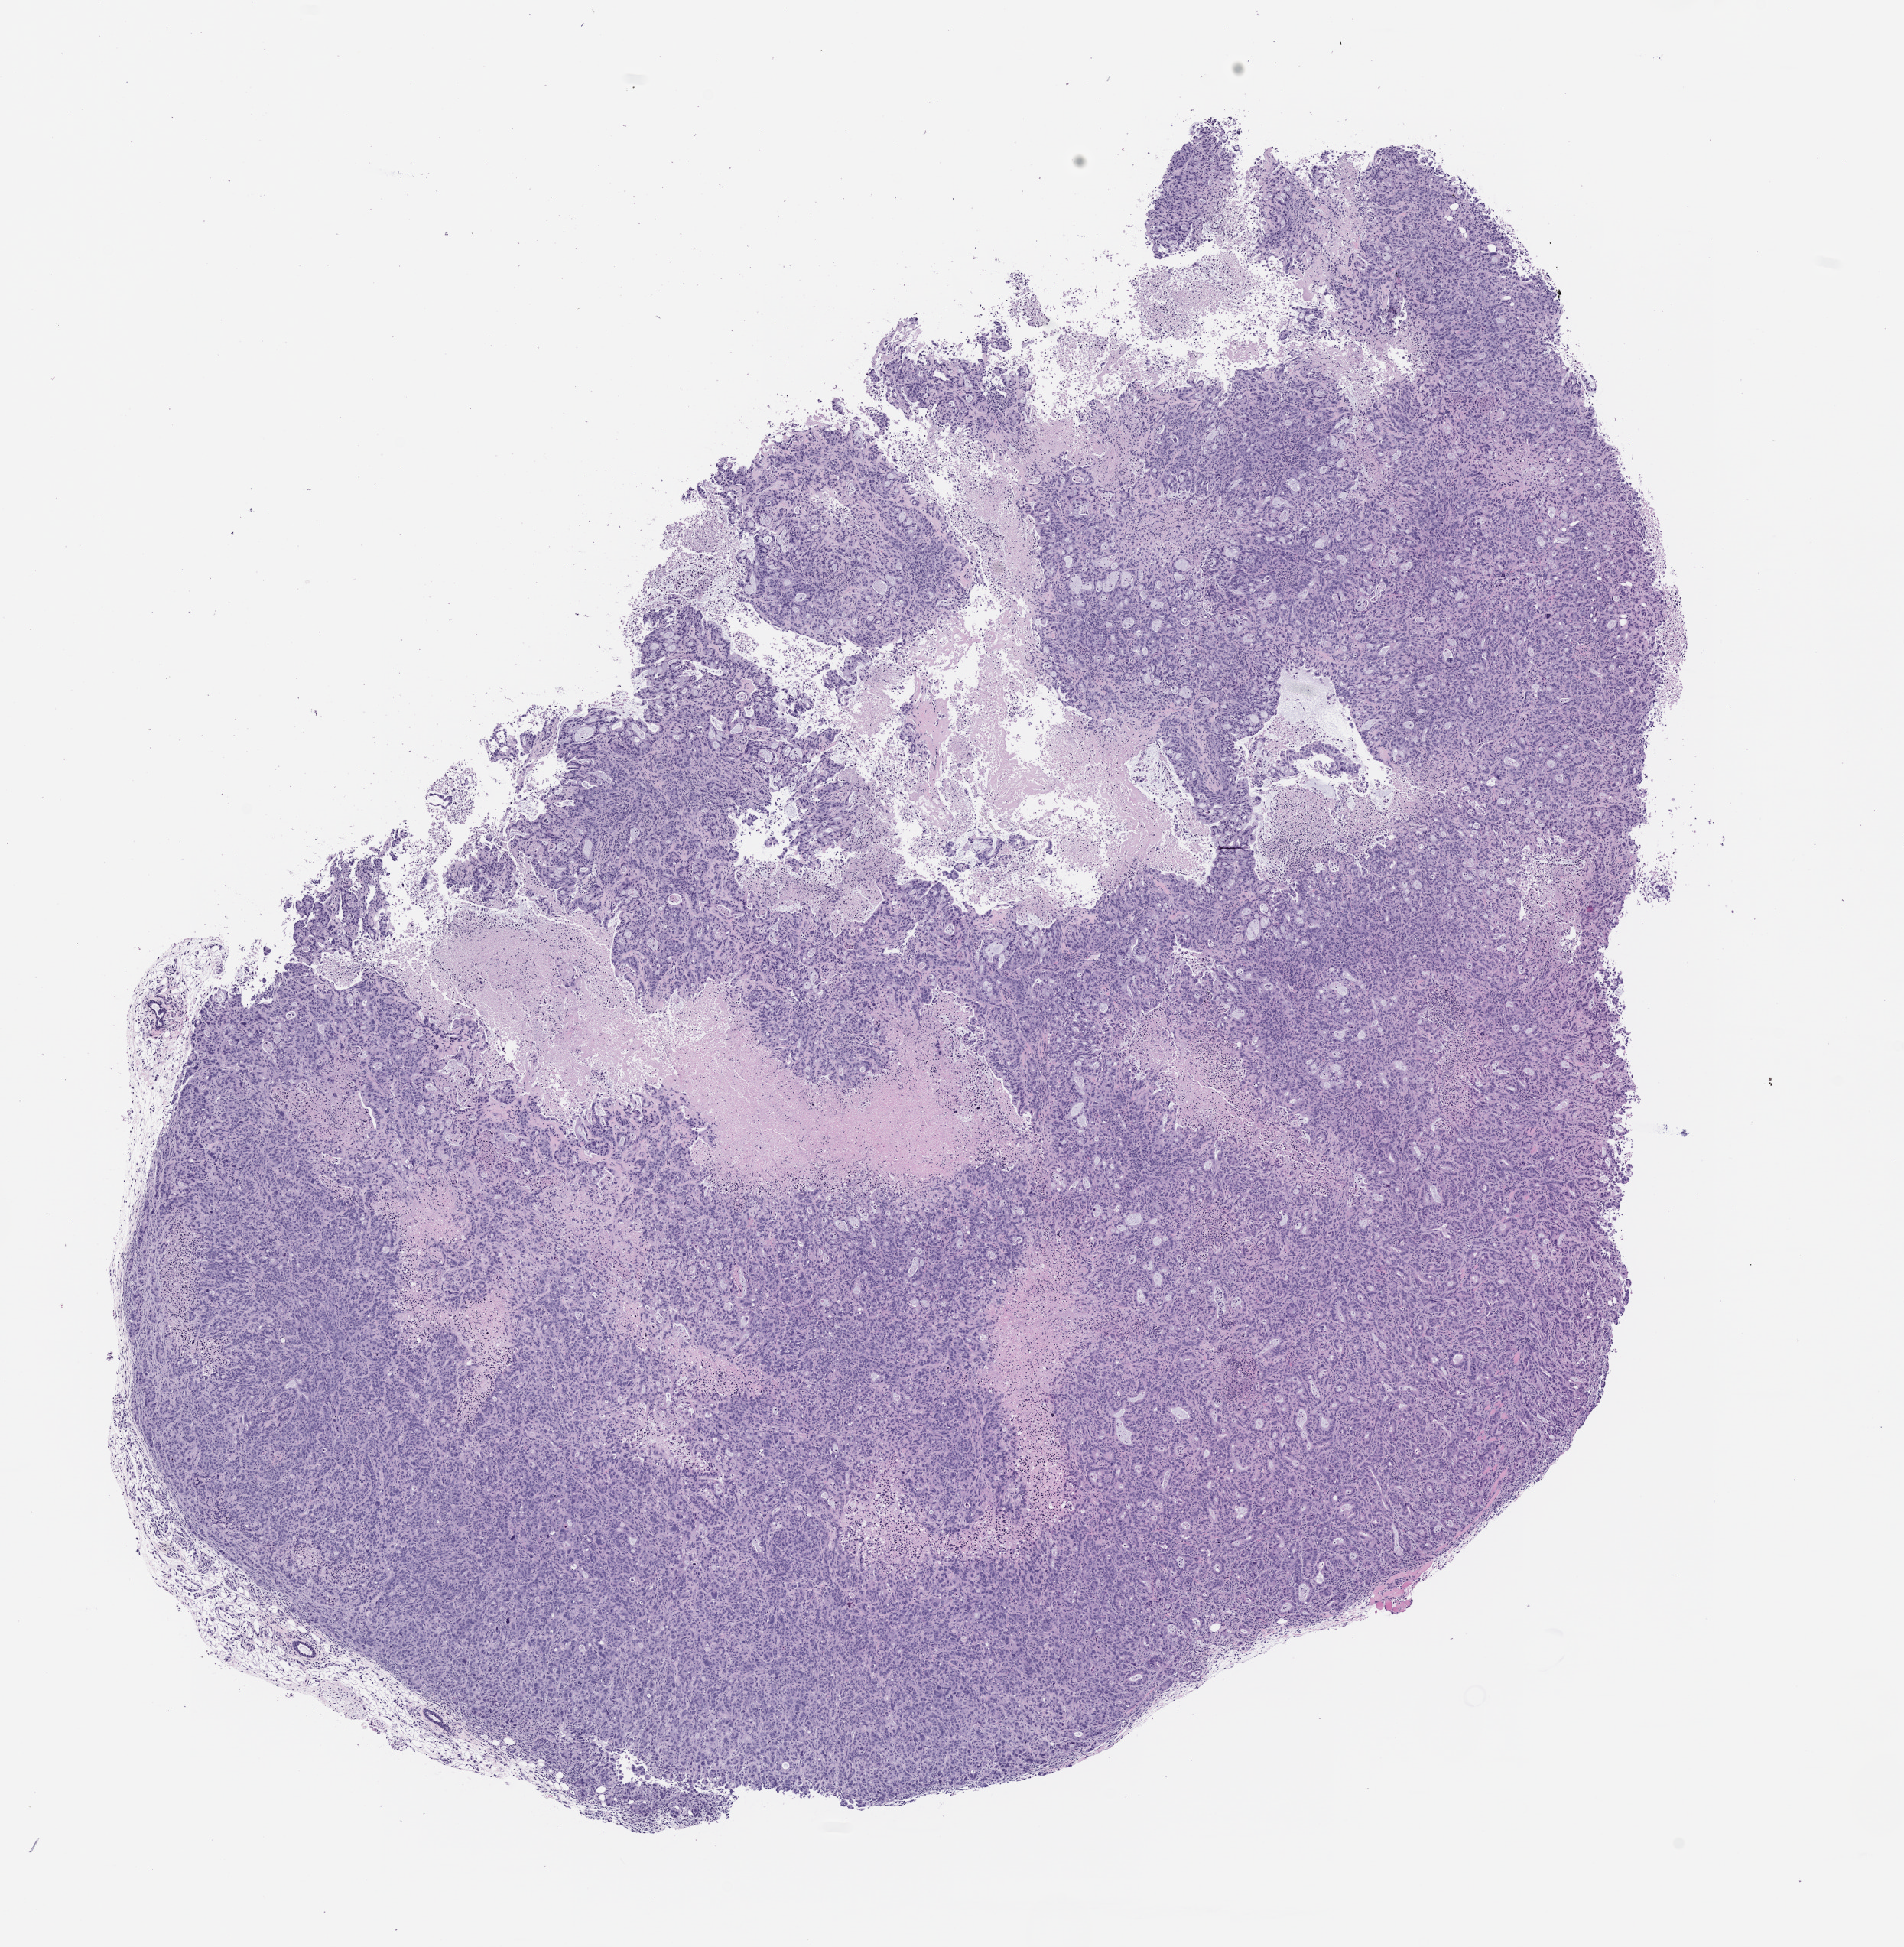
Haematoxylin and eosin whole-slide image of a patient-derived xenograft (PDX) tumor grown in a mouse, passage 4, a low-resolution overview of the entire scanned area, about 10.0 x 10.2 mm; FFPE section; tumor site category: pancreas.
* originating patient diagnosis: Pancreatic Adenocarcinoma